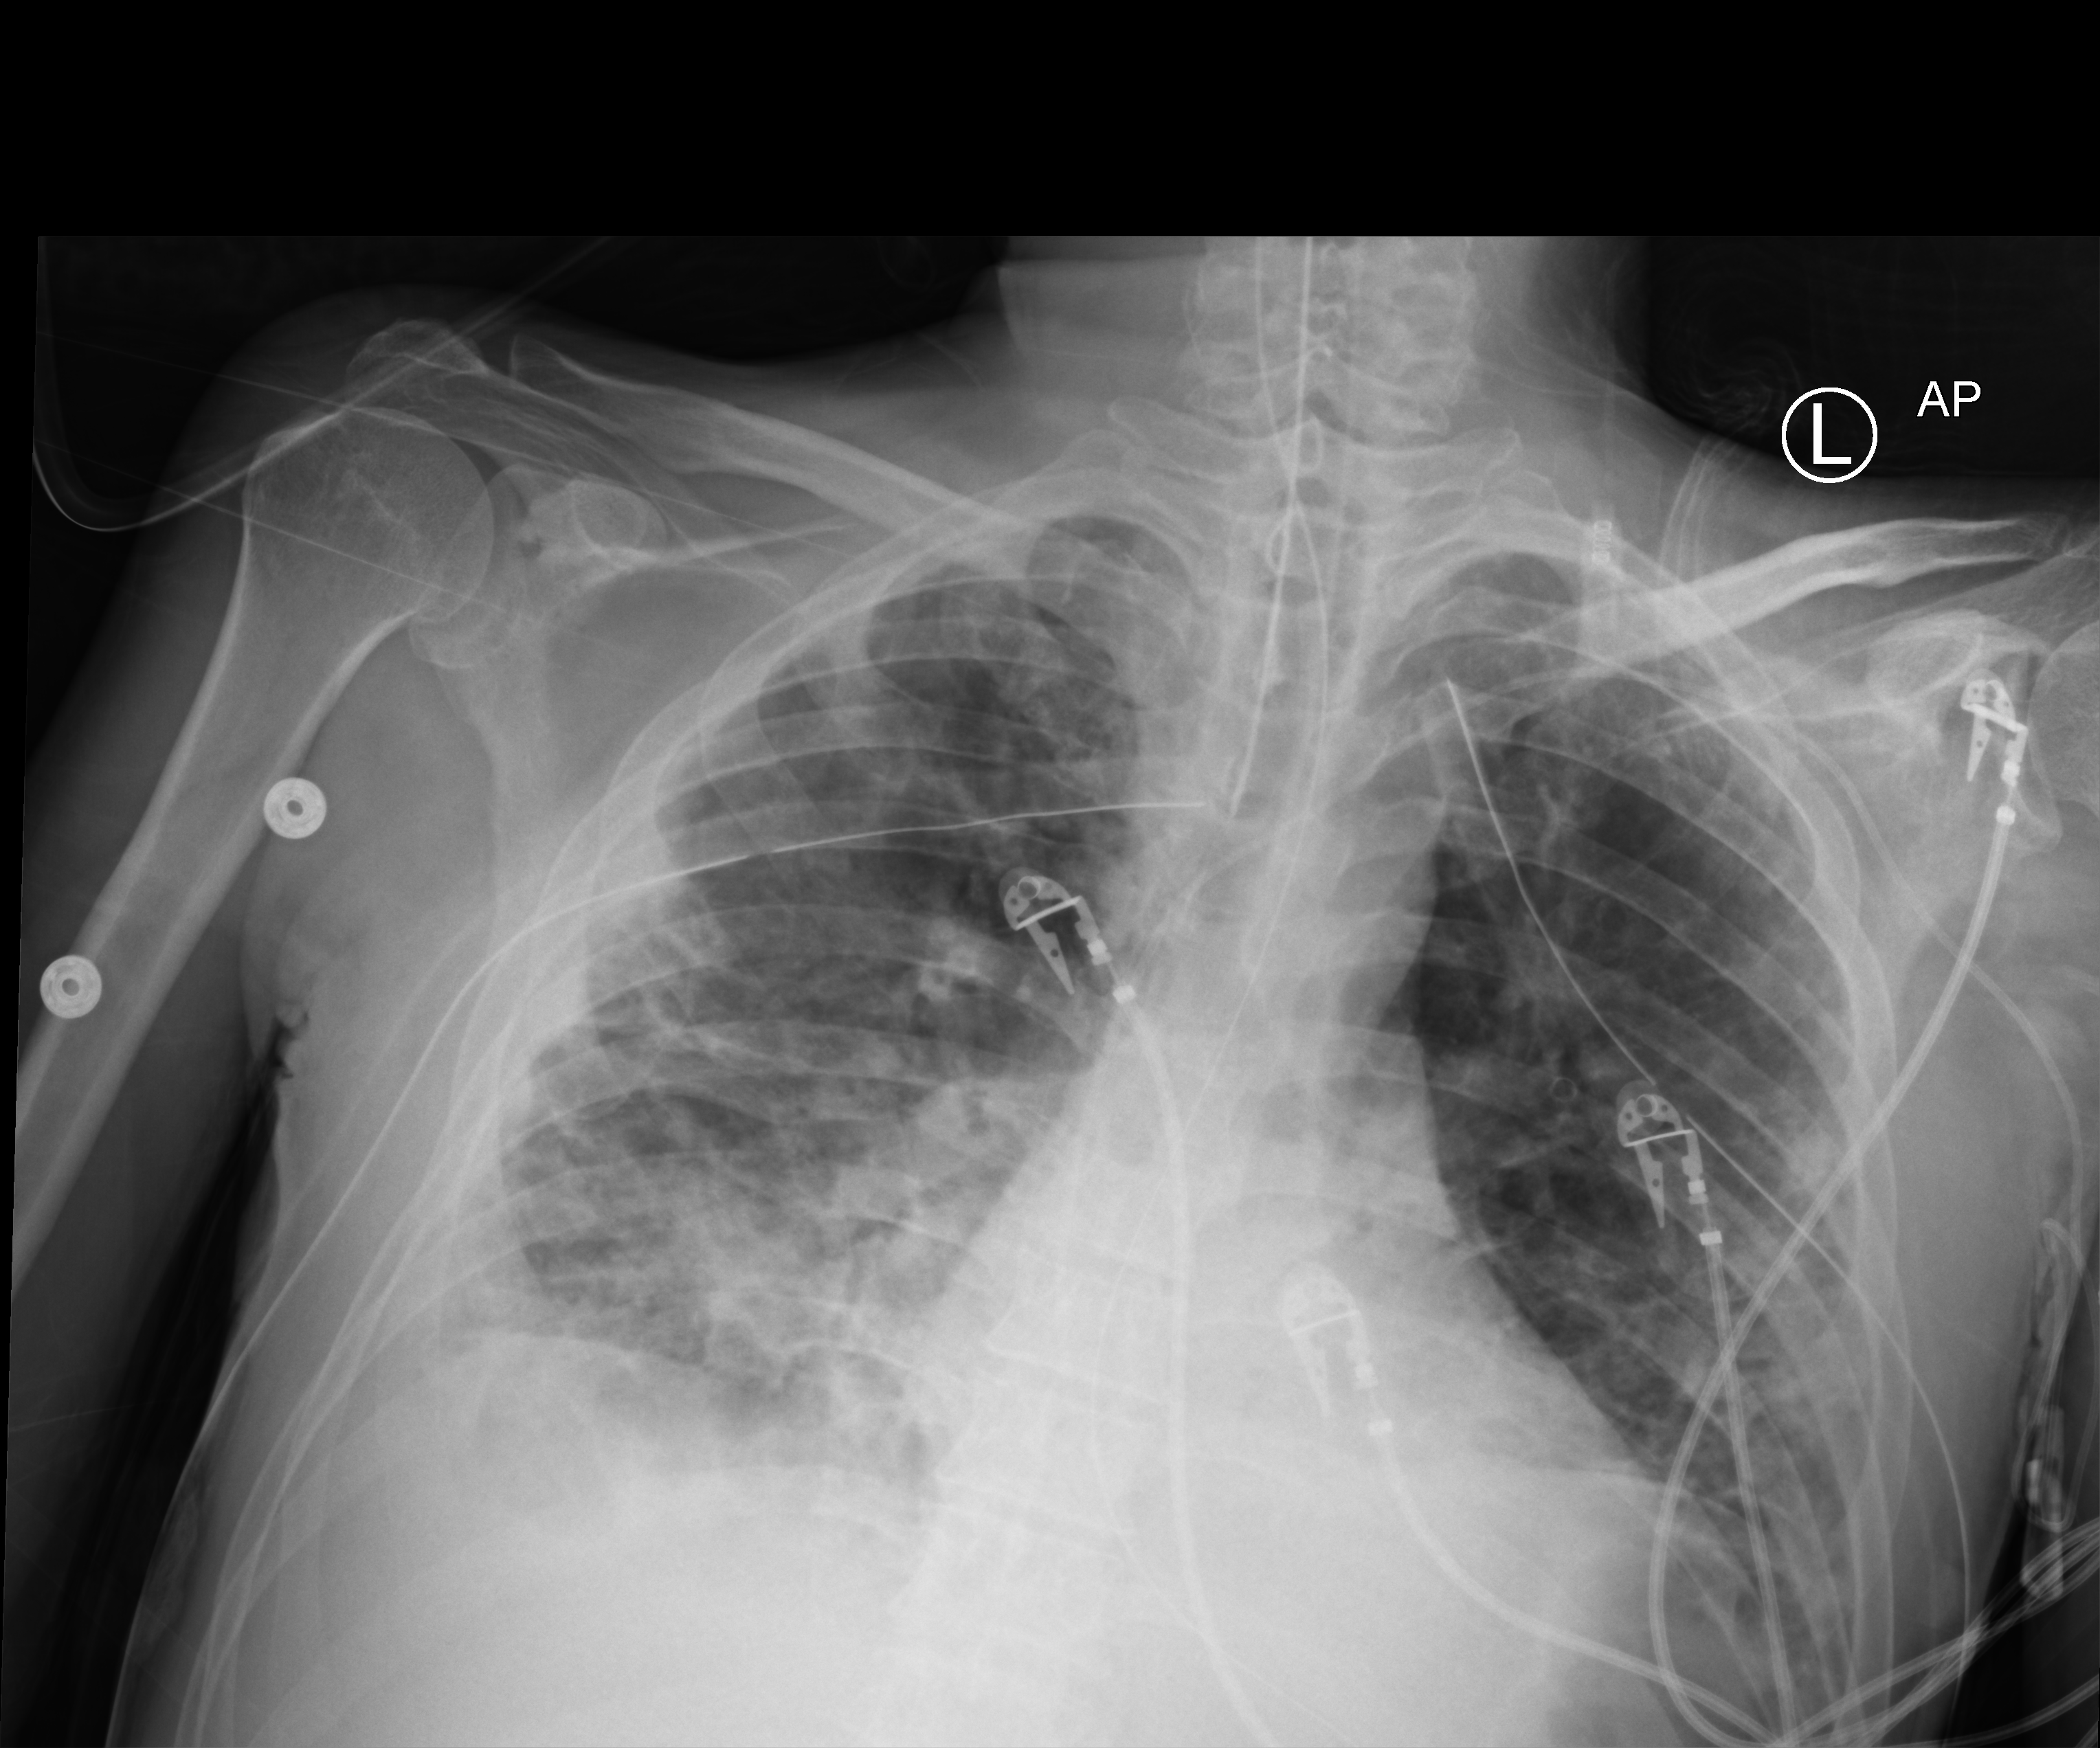
Portable chest radiograph, anteroposterior (AP) projection. Male patient hospitalised with COVID-19, age 18–59 years.
Admission-level facts for this patient (not findings on this image; timing relative to this image not recorded): COPD (admission record): no.